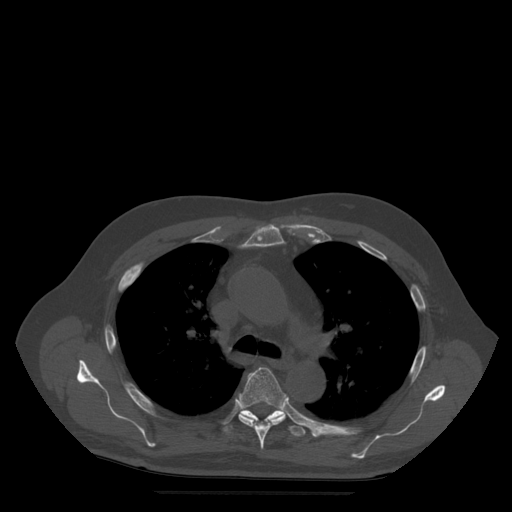
CT including the spine, one axial slice; position 367 of 522 along the scan axis; bone window (W 1800 / L 400 HU); 1.25 mm slice thickness; 512 × 512 image matrix, field of view 420 × 420 mm. Patient age 72 years. Case-level facts recorded for this patient, not image findings: primary cancer: prostate.
Structures marked on this image (semi-automatic segmentation, software-assisted and operator-edited):
- T5 vertebra: bounding box (x1, y1, x2, y2) in pixels: (238, 368, 288, 450)
- T6 vertebra: (225, 410, 306, 437)